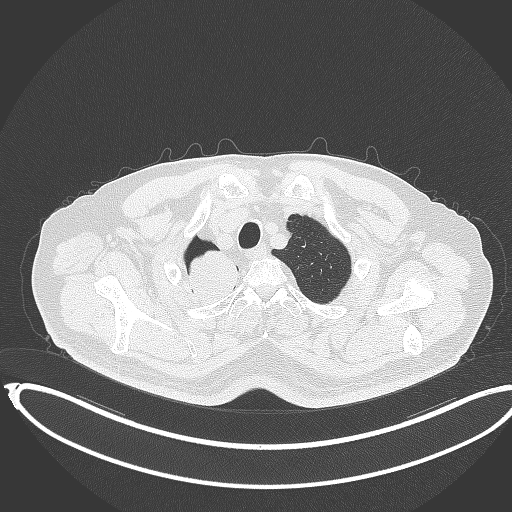
Chest CT, one axial slice. Reconstruction kernel B70f. 120 kVp. Lung window (W 1500 / L -600 HU). 512 × 512 image matrix, field of view 436 × 436 mm. Patient: male, 68 years. Case-level facts recorded for this patient, not image findings: clinical TNM (as recorded): T2a N0 M0.
Annotated regions visible in this slice (bounding box drawn by a radiologist):
- lung tumour (recorded histology: adenocarcinoma): box from (x=182, y=249) to (x=243, y=313) px